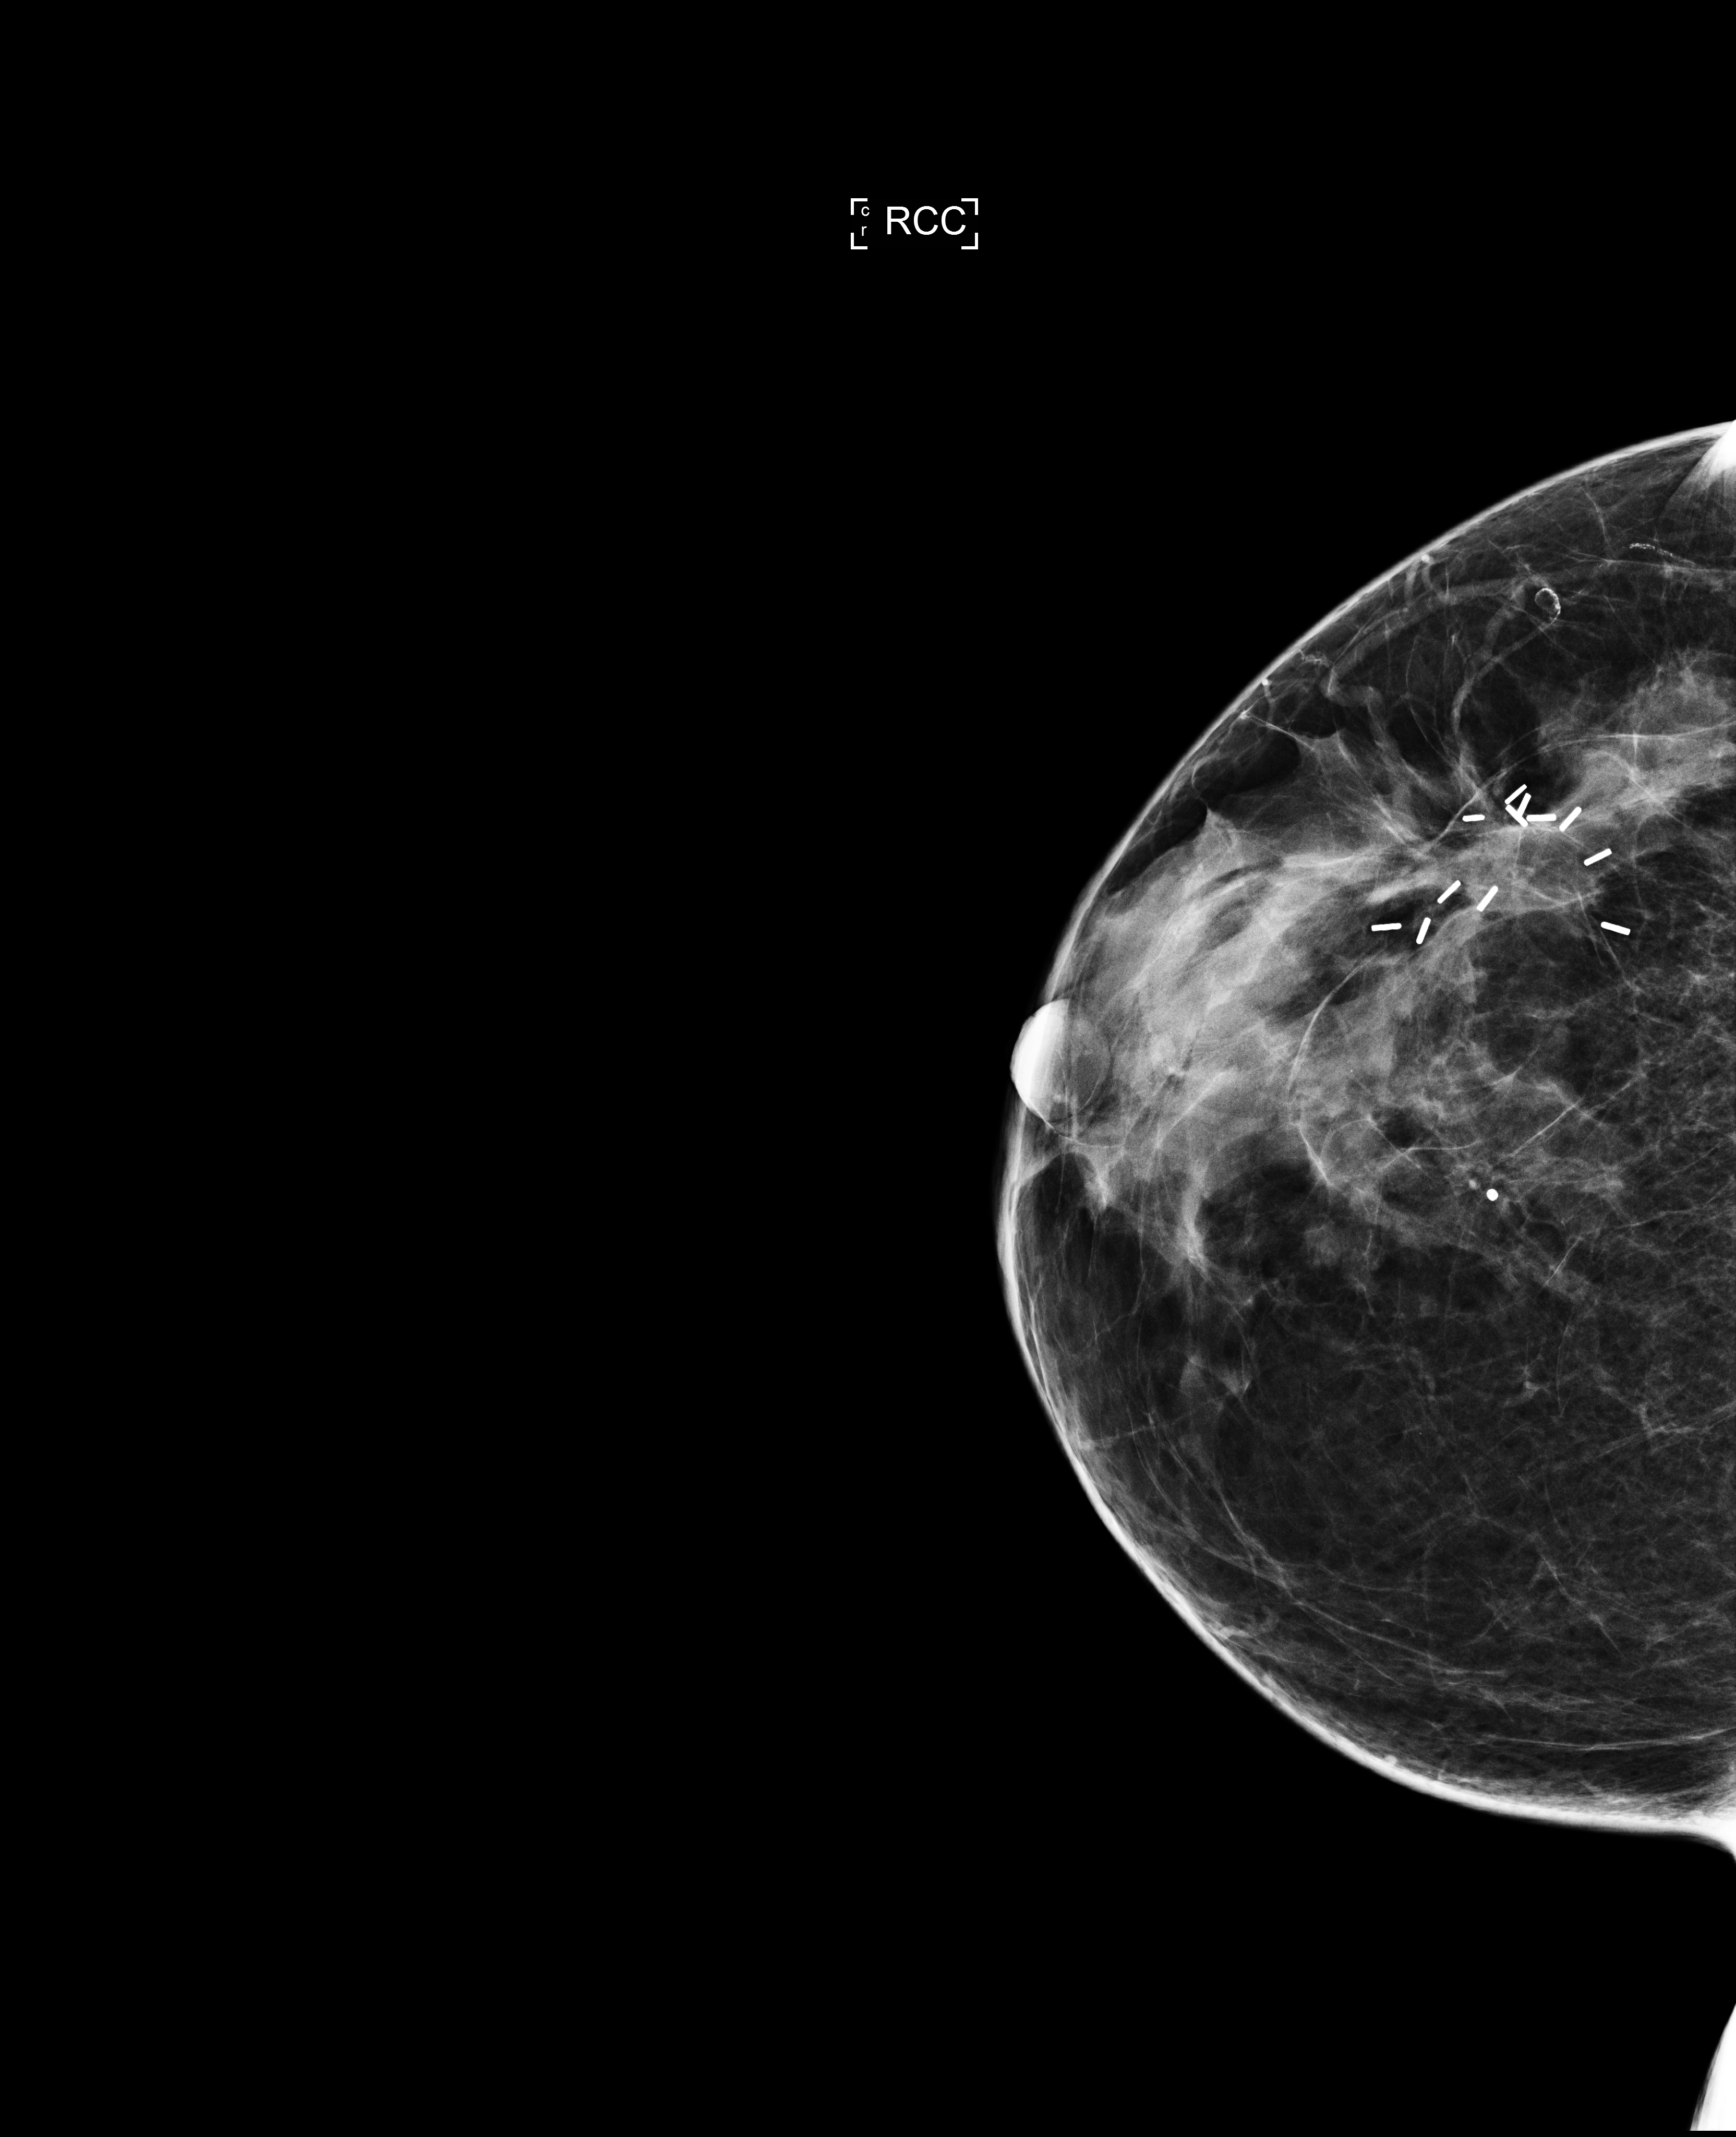
Annual screening mammography examination, compressed breast thickness 43 mm, system: Selenia Dimensions. Female patient, age 49 years.
Image type: full-field digital mammogram. Breast: right. Projection: CC view.